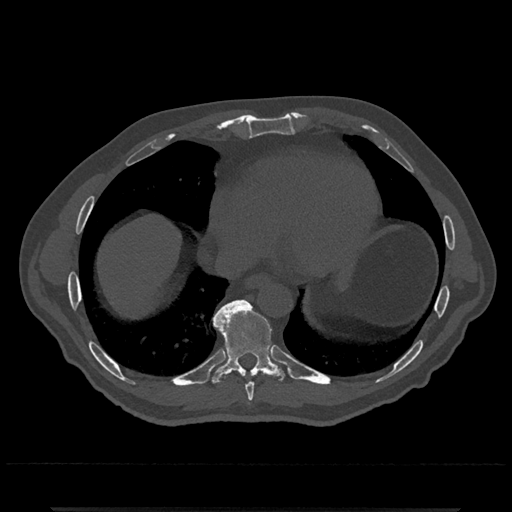
CT including the spine, one axial slice. Position 630 of 797 along the scan axis. 120 kVp. Bone window (W 1800 / L 400 HU). 0.5 mm slice thickness. 512 × 512 image matrix, field of view 393 × 393 mm. Patient: male, 67 years. From the clinical record (not read from this slice): primary cancer: prostate.
Outlined on this slice (semi-automatically segmented with operator editing):
- T8 vertebra: bounding box <246,383,254,402> (left, top, right, bottom; pixels)
- T9 vertebra: <209,300,292,385>